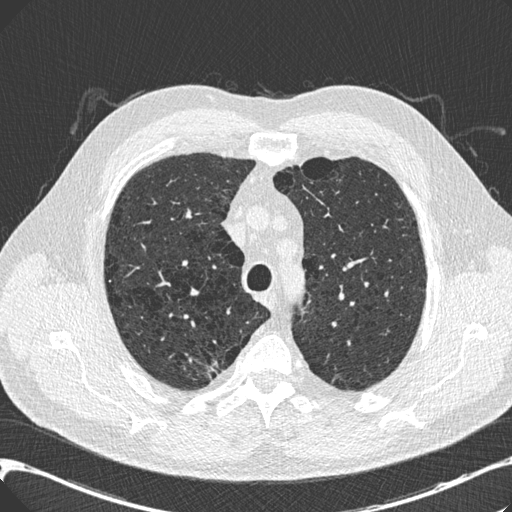
Low-dose screening chest CT, one axial slice; position 153 of 197 along the scan axis; reconstruction kernel B30f; 120 kVp; lung window (W 1500 / L -600 HU); 512 × 512 image matrix, field of view 367 × 367 mm.
Annotated regions visible in this slice (manually delineated by an expert):
- lesion 1 (tumor, upper lobe of right lung): bounding box (x1, y1, x2, y2) in pixels: (206, 360, 220, 379)